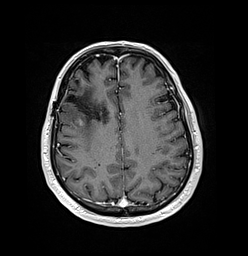
Brain MRI from a brain-tumour surgery series, one axial slice; position 57 of 176 along the scan axis; T1-weighted post-contrast; 248 × 256 image matrix, field of view 242 × 250 mm. Case-level facts recorded for this patient, not image findings: histopathology: Oligodendroglioma; WHO grade: 3; IDH mutation: yes; tumour location: Right Frontal.
Structures marked on this image (outlined manually by an expert reader):
- previous resection cavity: bounding box <65,95,78,105> (left, top, right, bottom; pixels)
- tumour: <73,113,85,128>